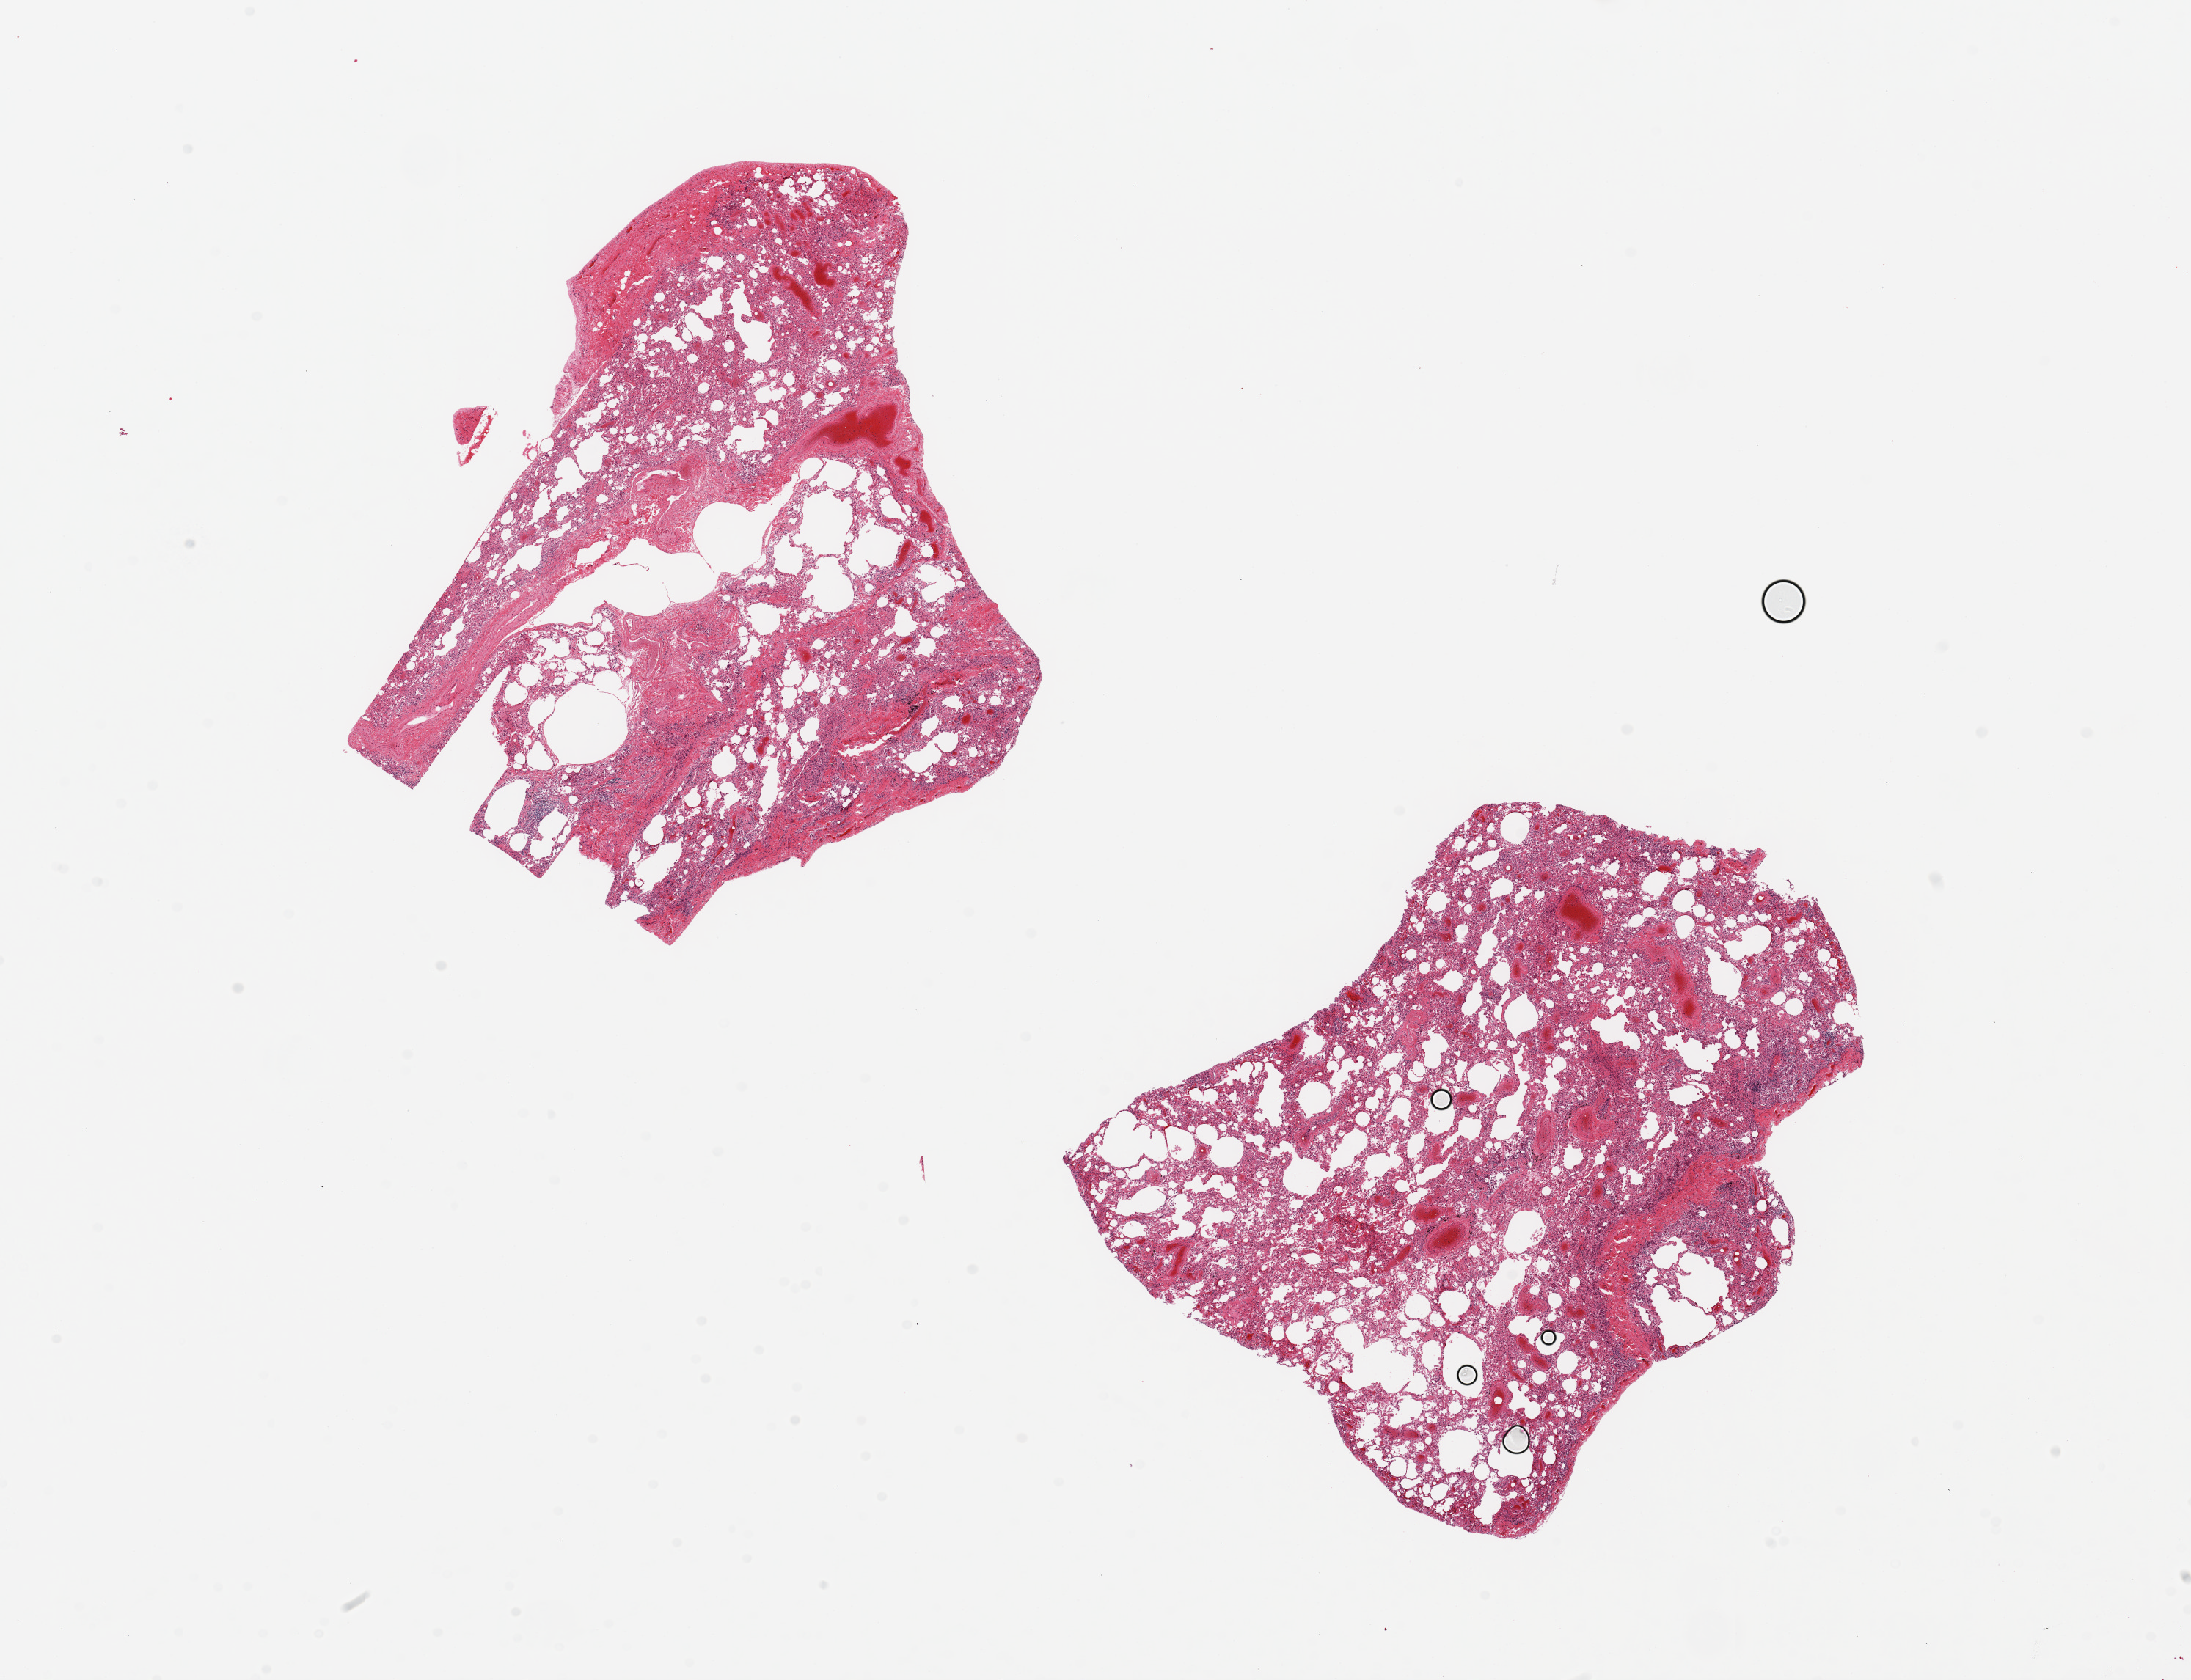
Hematoxylin and eosin (H&E) whole-slide image — shown as a low-resolution overview of the whole scanned area (about 23.6 x 18.1 mm, from a 20x scan), PAXgene-fixed paraffin-embedded (PFPE) section, target tissue: lung, tissue donor sample. Donor: male.
* pathologist's review note for this sample: 2 pieces, 8x7 & 8x6mm; focal emphysema, congestion